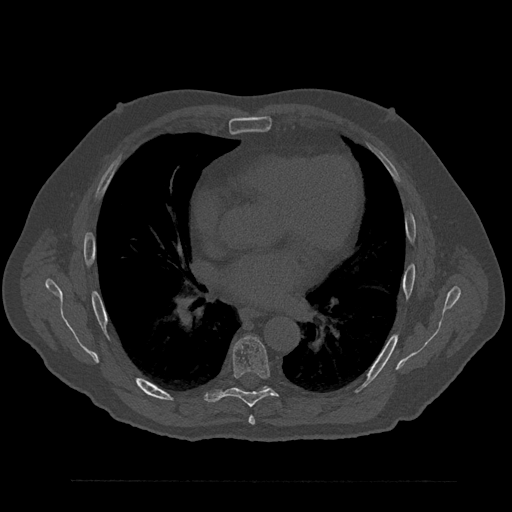
CT including the spine, one axial slice. Reconstruction kernel Br40s/3. Bone window (W 1800 / L 400 HU). 512 × 512 image matrix, field of view 430 × 430 mm. Male patient, age 61 years. Case-level facts recorded for this patient, not image findings: primary cancer: prostate.
Structures marked on this image (semi-automatically segmented with operator editing):
- T6 vertebra: bounding box (x1, y1, x2, y2) in pixels: (248, 416, 255, 425)
- T7 vertebra: (206, 336, 278, 408)